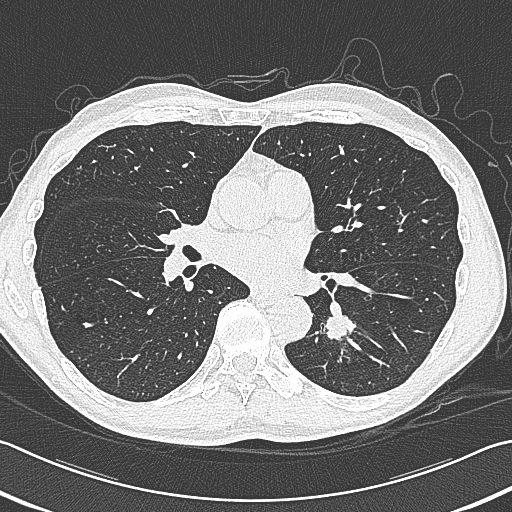
Axial slice from a low-dose chest CT screening exam, baseline annual screen, lung window (W 1500 / L -600 HU), slice 177 of 354 in the series, 512 × 512 image matrix. Male, age 59 years at enrolment. Former smoker at enrolment.
• Lesion marked by an expert reader, box from (x=312, y=295) to (x=375, y=353) px.
• The exam's reader record, not a measurement of the box and not confirmed to be the same lesion: non-calcified nodule or mass ≥4 mm, left lower lobe, 15 × 15 mm, smooth margins, soft tissue attenuation.
• Later outcome: lung cancer diagnosed 17 days after this screen — squamous cell carcinoma, large cell, nonkeratinizing, NOS, left lower lobe, poorly differentiated (G3), stage IB (AJCC 6th edition), 31 mm at pathology.